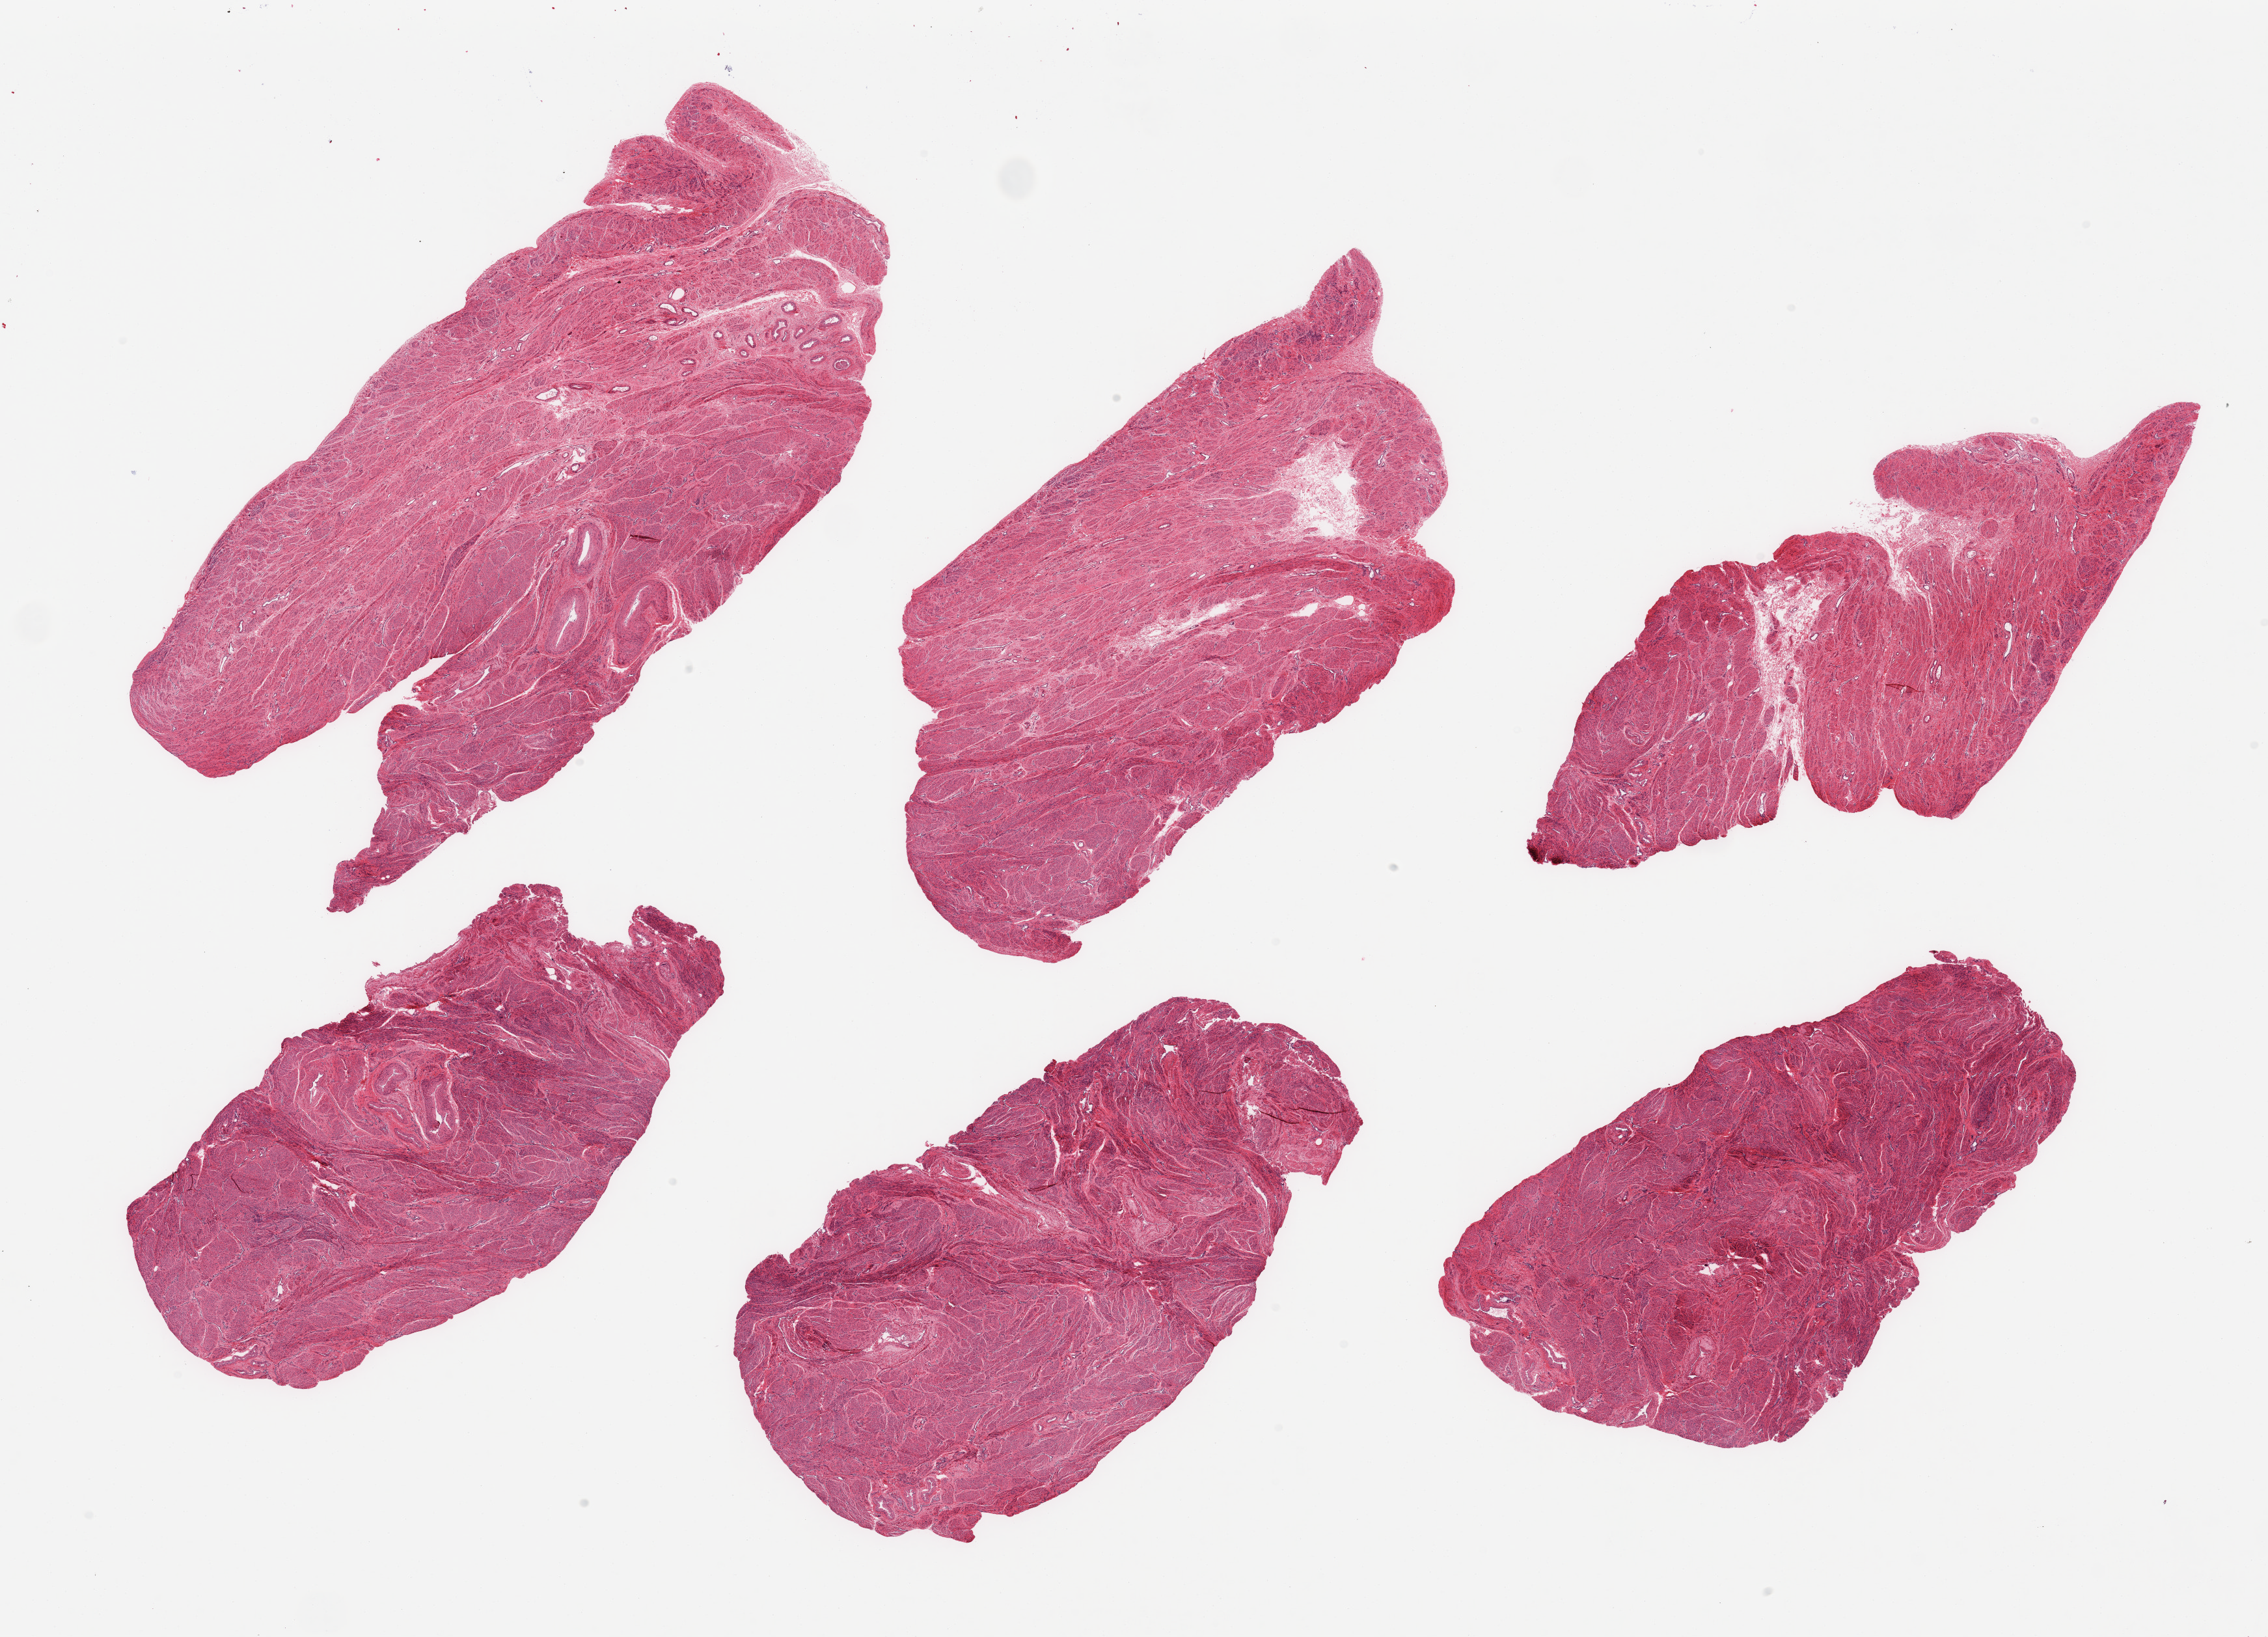
Digitized H&E-stained section, whole scanned area (about 27.6 x 19.9 mm) shown as a low-resolution overview. PAXgene-fixed paraffin-embedded (PFPE) section. Target tissue: uterus. Donor tissue sample. Female donor.
Review note (as recorded): 6 pieces; myometrium only in this section.